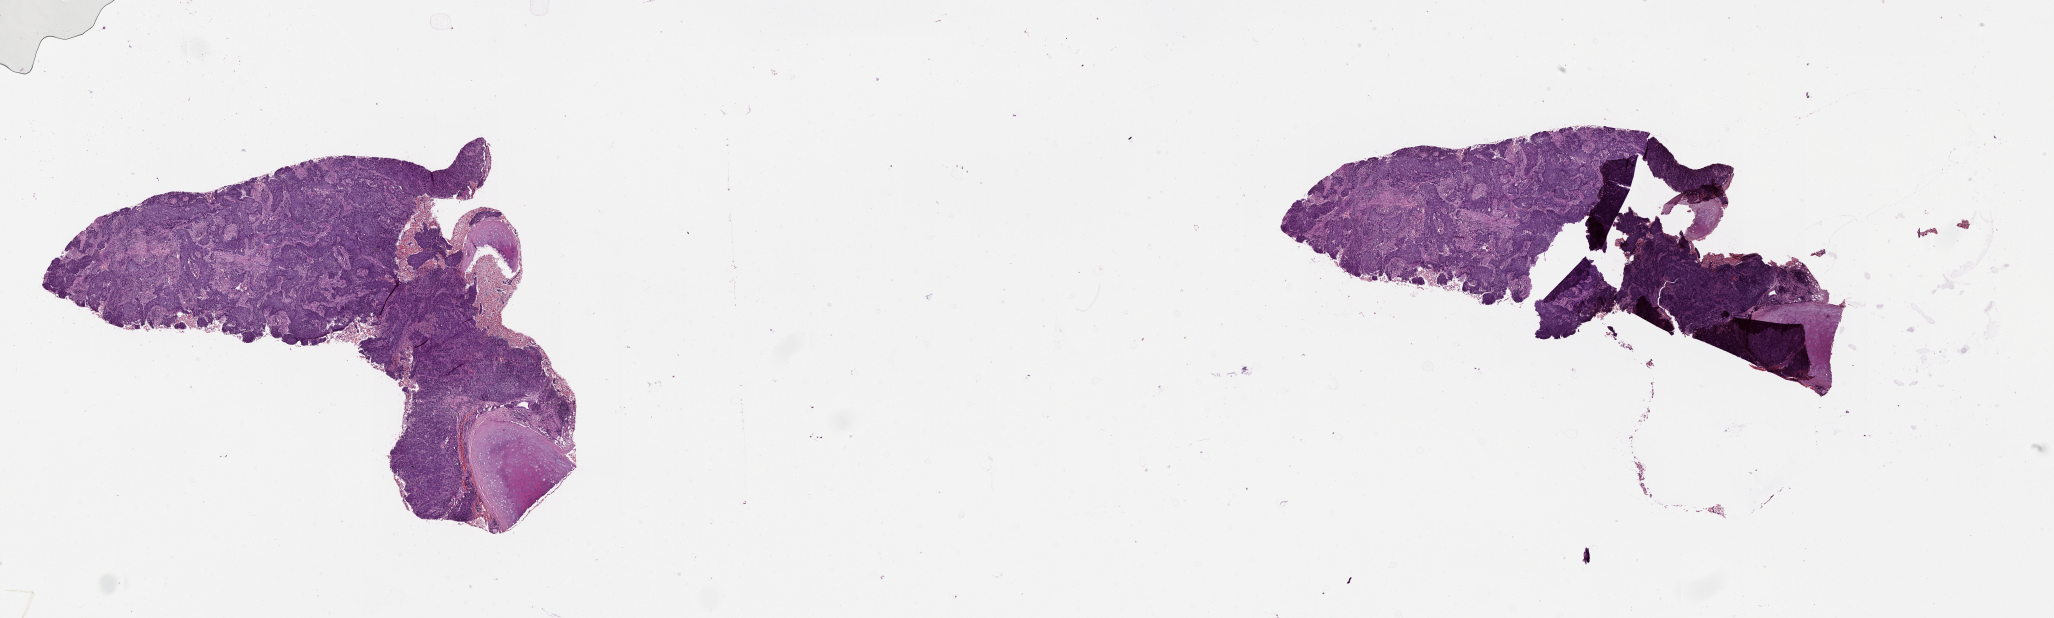
Whole-slide histology image, Hematoxylin and eosin (H&E) stained — a low-resolution overview of the entire scanned area, about 33.1 x 10.0 mm (slide scanned at 20x); tumour tissue sample, lung. 53-year-old male patient.
- patient diagnosis (cohort enrolment): squamous cell carcinoma (lung)